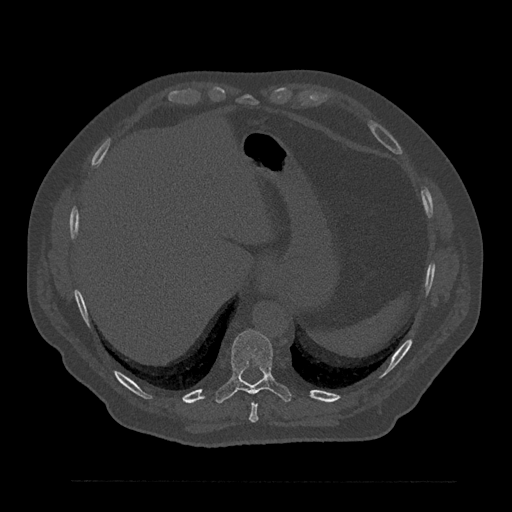
CT including the spine, one axial slice; slice 358 of 797 in the series (ordered by position); 120 kVp; bone window (W 1800 / L 400 HU); 512 × 512 image matrix, field of view 430 × 430 mm. Patient: male, 61 years. Case-level facts recorded for this patient, not image findings: primary cancer: prostate.
Structures marked on this image (semi-automatically segmented with operator editing):
- T10 vertebra: box from (x=215, y=330) to (x=292, y=403) px
- T9 vertebra: (x=249, y=402)–(x=258, y=423)